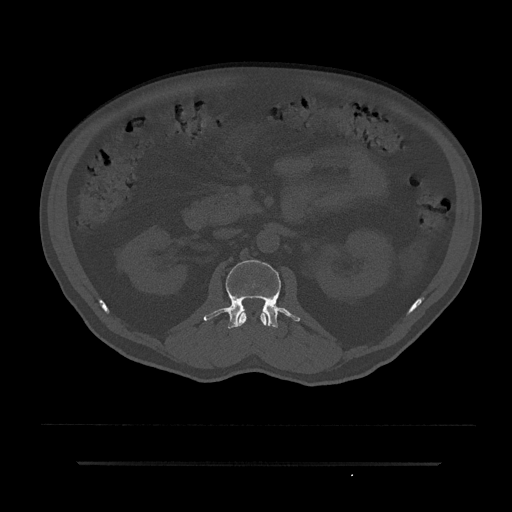
CT including the spine, one axial slice; slice 94 of 797 in the series (ordered by position); bone window (W 1800 / L 400 HU); 512 × 512 image matrix. Male patient, age 59 years. Case-level facts recorded for this patient, not image findings: primary cancer: bile ducts; vertebrae with lytic lesions (as recorded): T10.
Structures marked on this image (semi-automatic segmentation, software-assisted and operator-edited):
- L1 vertebra: box from (x=238, y=311) to (x=267, y=326) px
- L2 vertebra: (x=203, y=260)–(x=300, y=329)